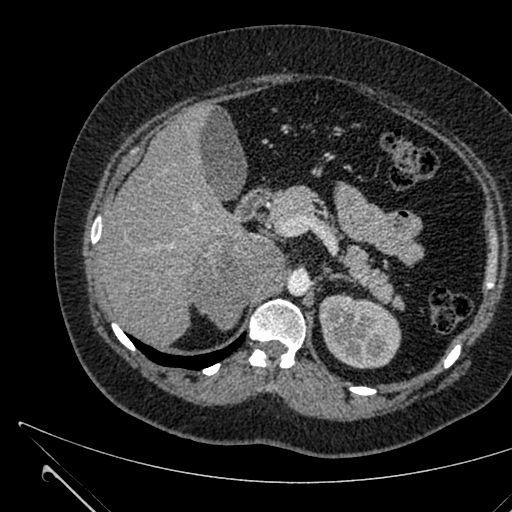
Contrast-enhanced abdominal CT, one axial slice; position 424 of 731 along the scan axis; intravenous contrast given; soft-tissue window (W 400 / L 40 HU); 1 mm slice thickness; 512 × 512 image matrix. Female patient, age 36 years. Case-level facts recorded for this patient, not image findings: diagnosis: adrenocortical carcinoma; tumour side: right adrenal; tumour size at pathology: 10 cm; Ki-67 index: 20 %; stage (as recorded): 4.
Structures marked on this image (semi-automatically segmented with operator editing):
- mass: box from (x=191, y=233) to (x=285, y=328) px